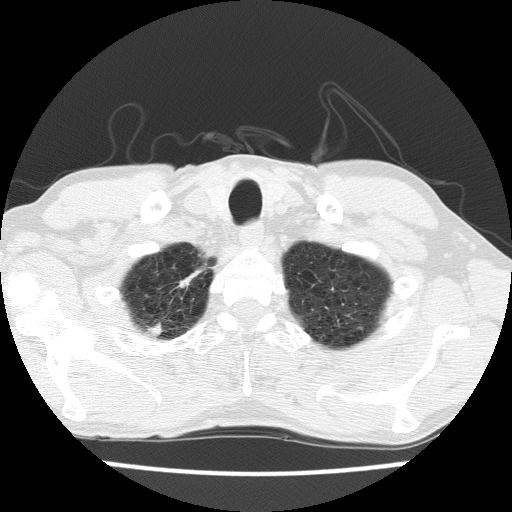
Axial slice from a low-dose chest CT screening exam. Second screening round (one year after baseline). Lung window (W 1500 / L -600 HU). 2 mm slice thickness. Slice 15 of 175 in the series. 512 × 512 image matrix, field of view 326 × 326 mm. Male participant, aged 63 years at enrolment.
Expert reader's lesion annotation, bounding box [x1, y1, x2, y2] px = [137, 264, 209, 333]. No non-calcified nodule or mass ≥4 mm was recorded by the screening reader at this exam. Official screen result: negative screen, minor abnormalities not suspicious for lung cancer.